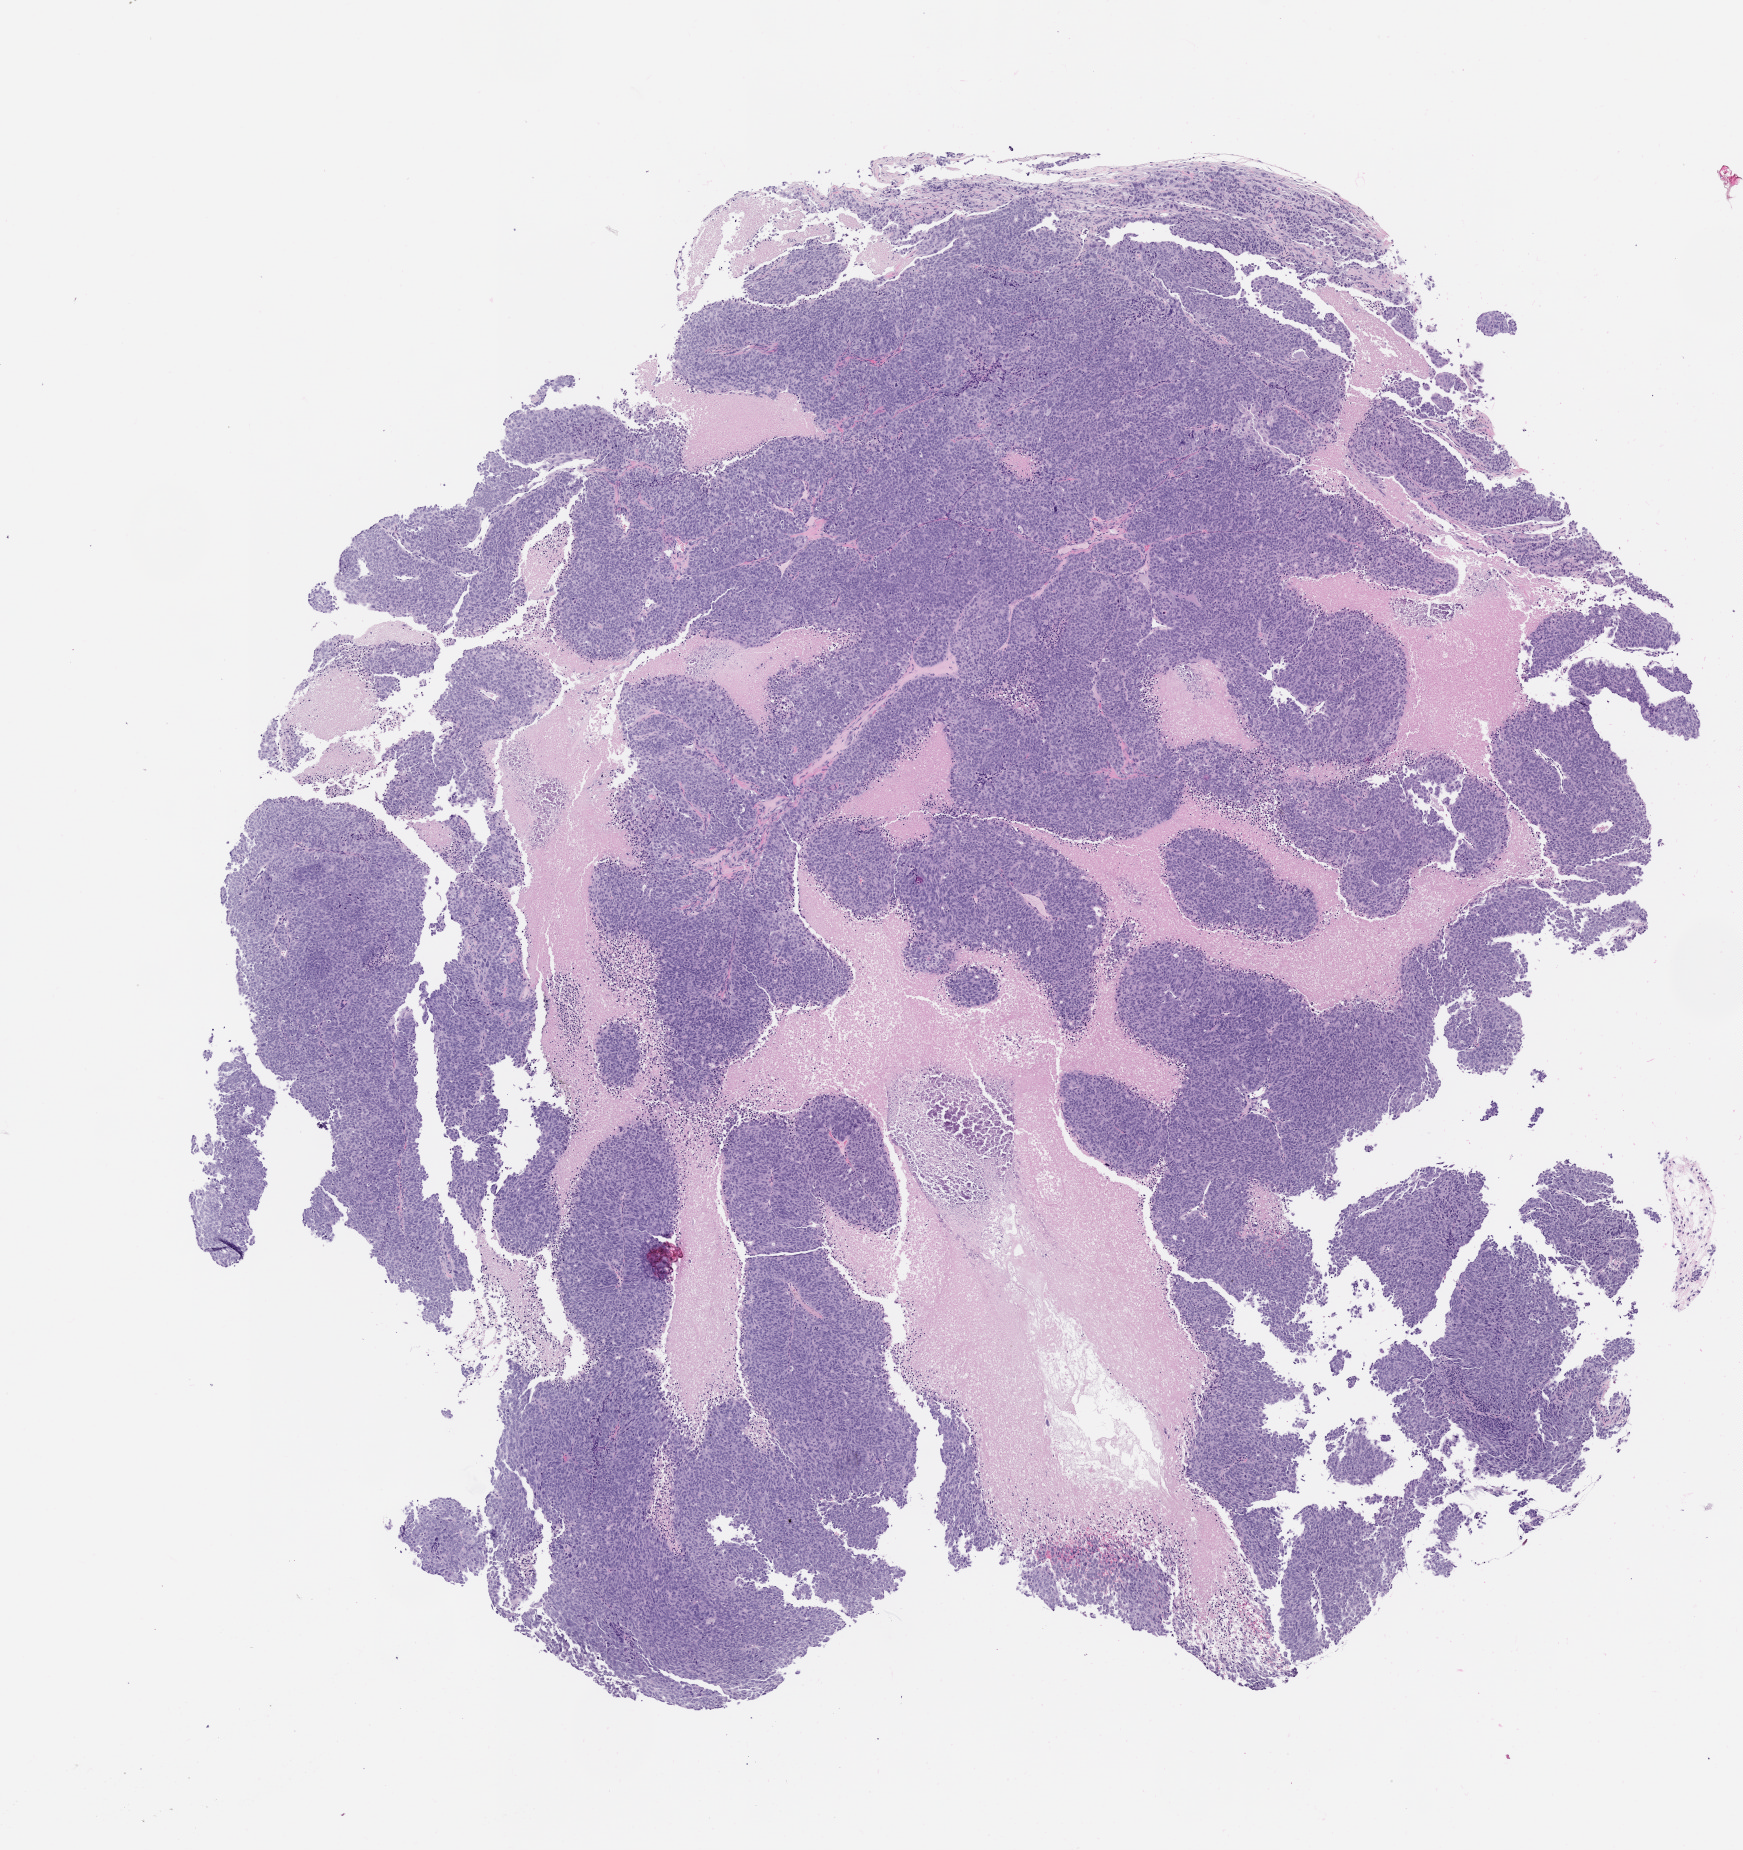
Whole-slide image, haematoxylin and eosin: patient-derived xenograft (human tumor grown in a mouse), passage 1, whole scanned area (about 7.0 x 7.4 mm) shown as a low-resolution overview, formalin-fixed paraffin-embedded section, originating tumor site category: cervix.
Originating patient diagnosis: Cervical Adenocarcinoma.